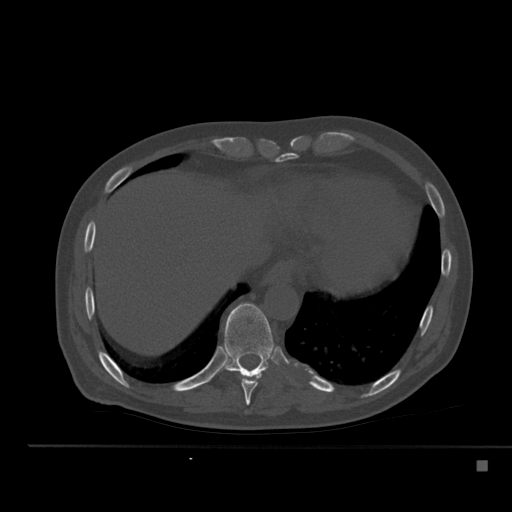
CT including the spine, one axial slice. Position 276 of 517 along the scan axis. Reconstruction kernel Br40s. Bone window (W 1800 / L 400 HU). 512 × 512 image matrix, field of view 408 × 408 mm. Patient: male, 70 years. From the clinical record (not read from this slice): primary cancer: renal.
Structures marked on this image (semi-automatically segmented with operator editing):
- T10 vertebra: bounding box (x1, y1, x2, y2) in pixels: (224, 303, 277, 377)
- T9 vertebra: (239, 371, 262, 405)